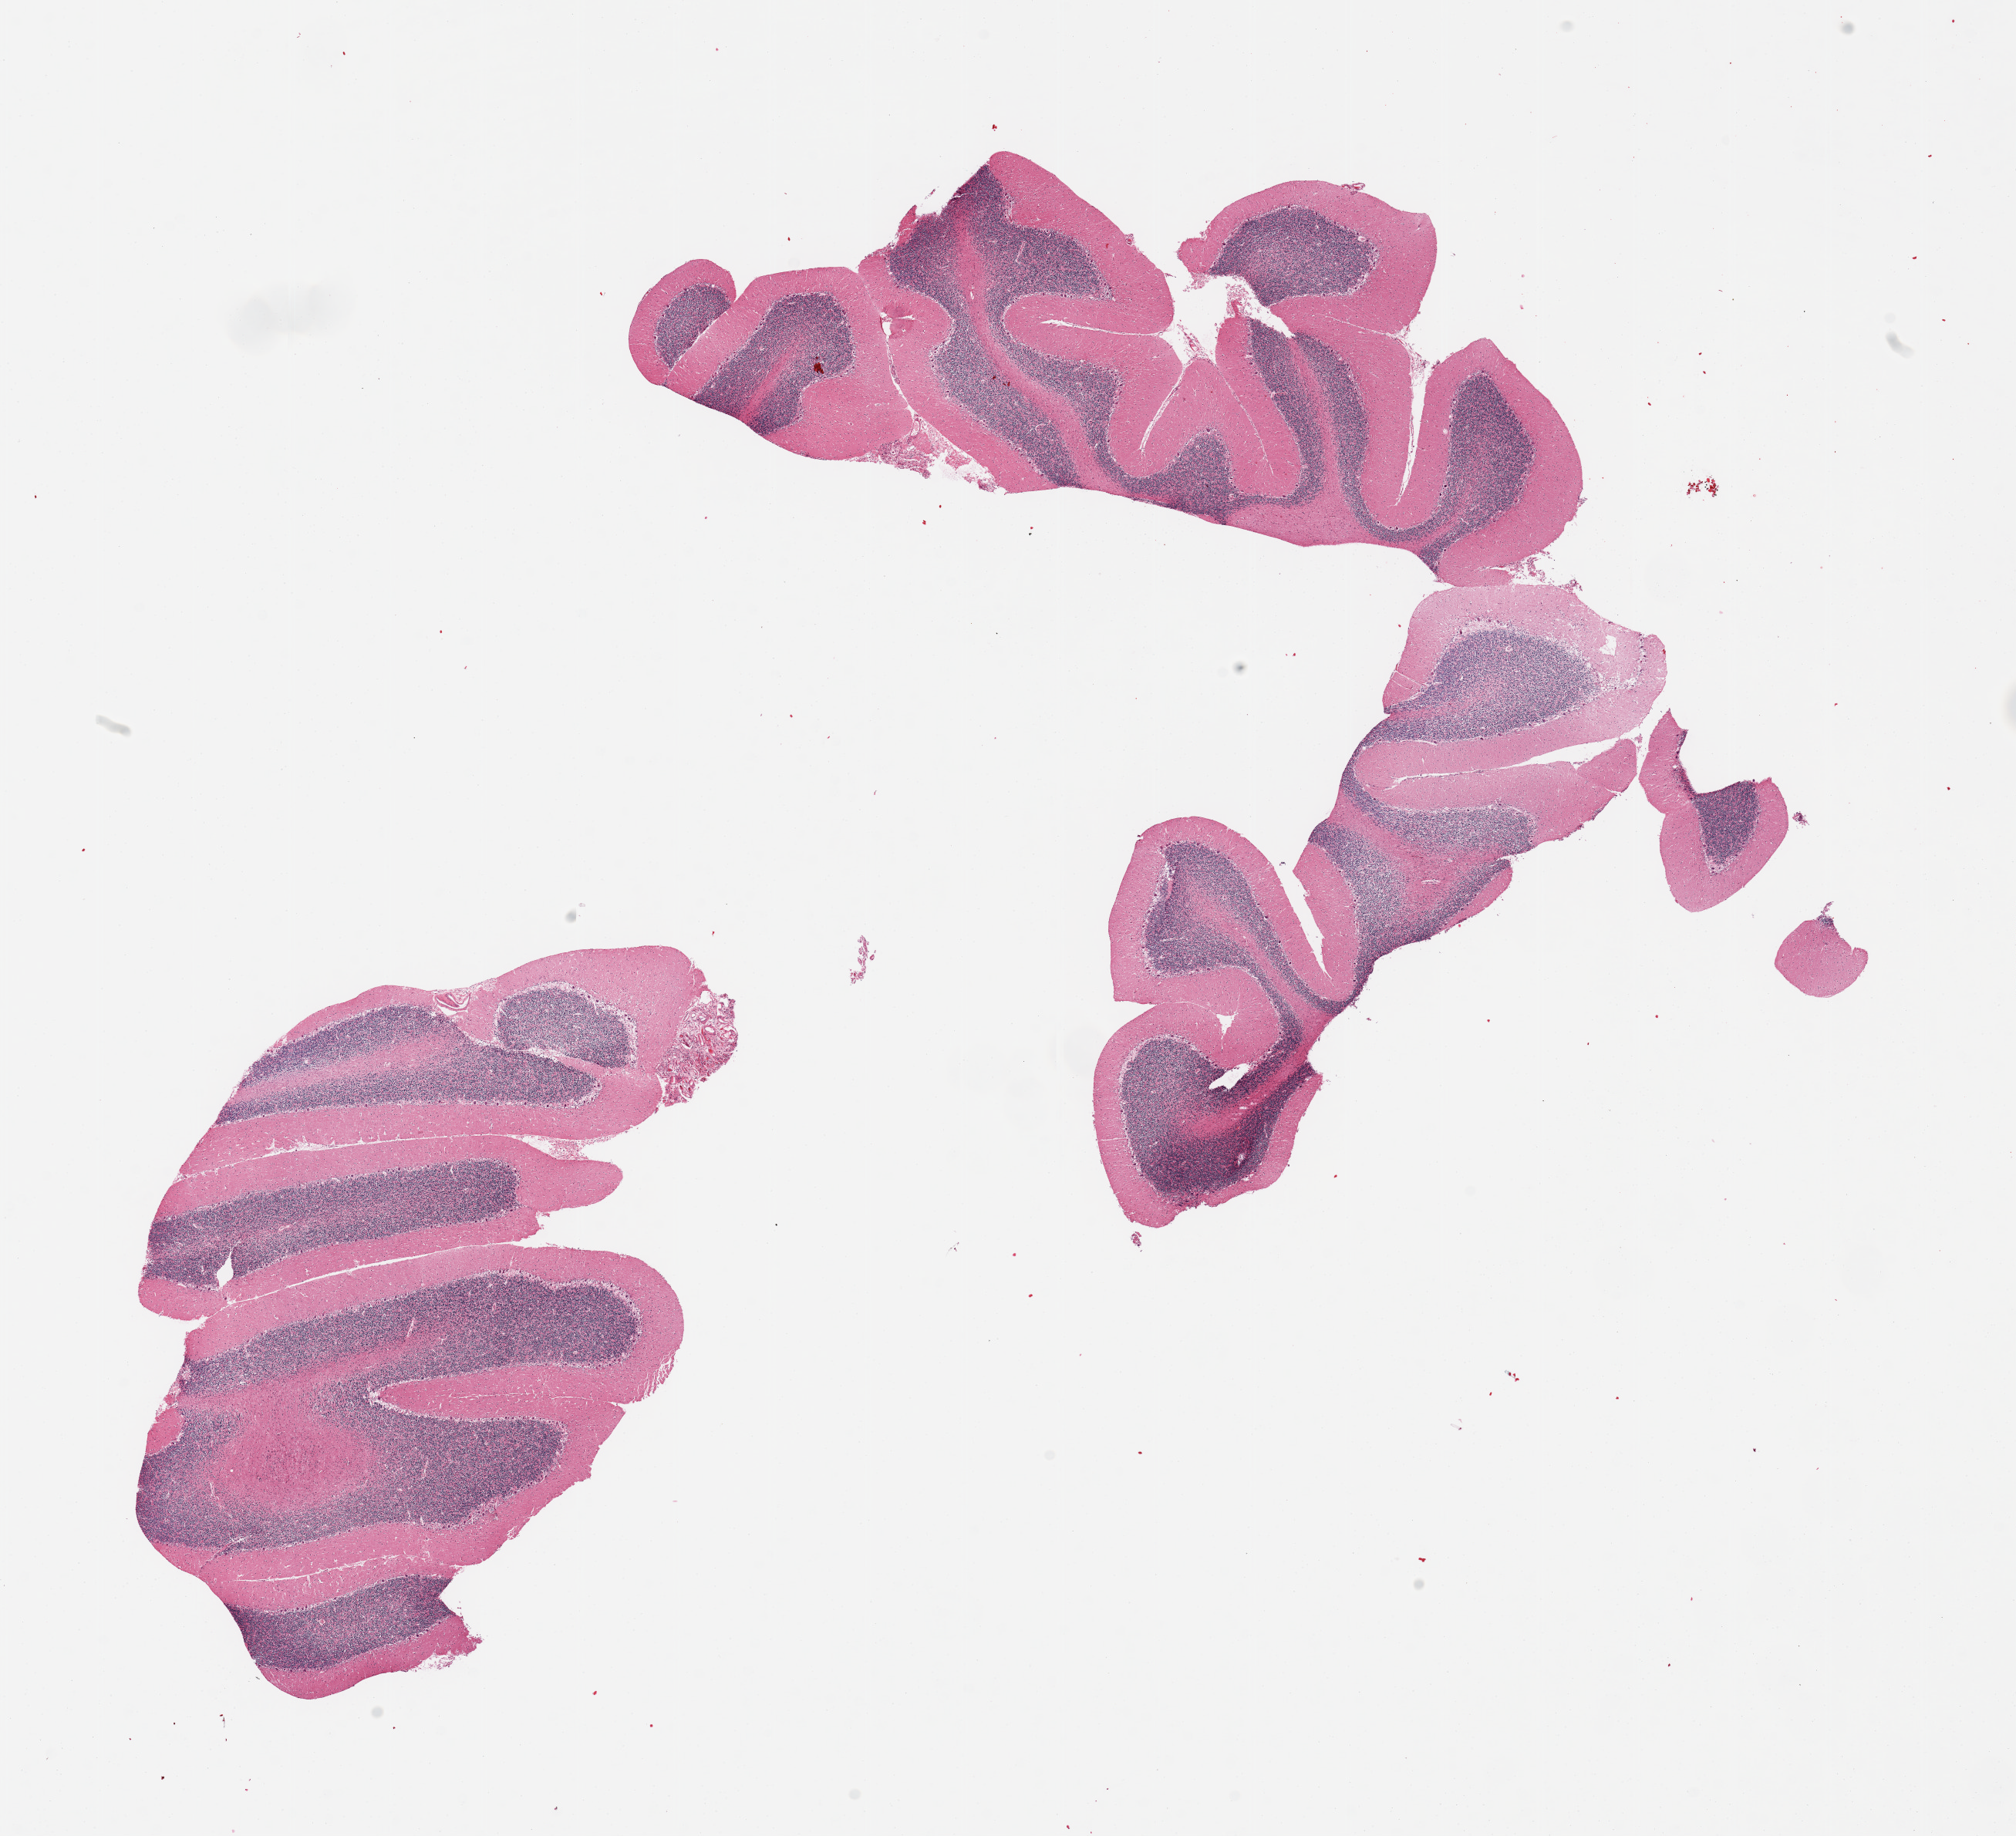
Whole-slide image, H&E stain, shown as a low-resolution overview of the whole scanned area (about 20.7 x 18.8 mm, from a 20x scan). PAXgene-fixed, paraffin-embedded tissue. Target tissue: cerebellum. Tissue donor sample. Donor: female.
* reviewer comment on this tissue sample: 3 pieces